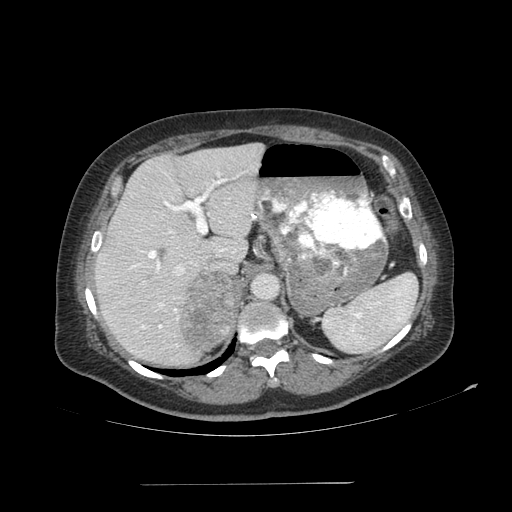
Contrast-enhanced abdominal CT, one axial slice. Position 74 of 113 along the scan axis. Reconstruction kernel SOFT. Soft-tissue window (W 400 / L 40 HU). 512 × 512 image matrix, field of view 440 × 440 mm. Patient: female, 67 years. From the clinical record (not read from this slice): diagnosis: adrenocortical carcinoma; tumour side: right adrenal; tumour size at pathology: 9.8 cm; Ki-67 index: 59 %; stage (as recorded): 4.
Structures marked on this image (semi-automatically segmented with operator editing):
- mass: bounding box [x1, y1, x2, y2] px = [181, 272, 237, 351]